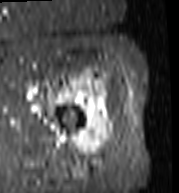
MRI of an extremity soft-tissue mass, one axial slice; position 89 of 103 along the scan axis; STIR; MR volume resampled by the dataset authors to the PET/CT grid (not the native acquisition matrix); 179 × 193 image matrix, field of view 175 × 188 mm. Female patient. Case-level facts recorded for this patient, not image findings: histological type: undifferentiated – high grade; grade: high; site of the primary tumour: left thigh.
Annotated regions visible in this slice (expert contour drawn on MRI and transferred to this co-registered scan by the dataset authors):
- gross tumour volume including surrounding oedema: bounding box <66,73,115,156> (left, top, right, bottom; pixels)
- gross tumour volume (mass): <68,73,112,156>